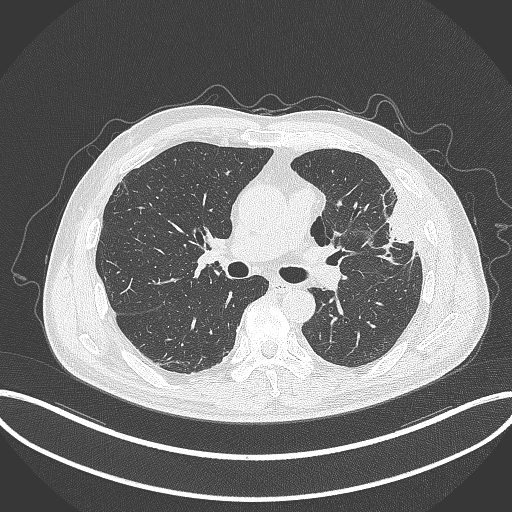
Chest CT, one axial slice. Position 196 of 382 along the scan axis. Reconstruction kernel B70f. Lung window (W 1500 / L -600 HU). 1 mm slice thickness. 512 × 512 image matrix, field of view 415 × 415 mm. Male patient, age 64 years. Case-level facts recorded for this patient, not image findings: clinical TNM (as recorded): T4 N1 M0.
Outlined on this slice (rectangle marked by the reading radiologist):
- lung tumour (recorded histology: adenocarcinoma): bounding box (x1, y1, x2, y2) in pixels: (375, 188, 418, 261)